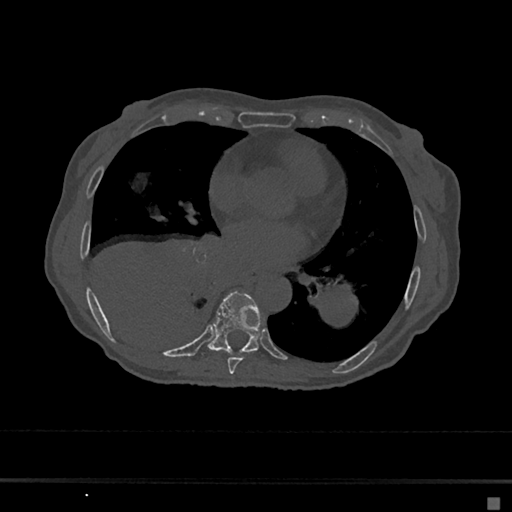
CT including the spine, one axial slice; position 344 of 797 along the scan axis; reconstruction kernel Br40s/3; 120 kVp; bone window (W 1800 / L 400 HU); 512 × 512 image matrix, field of view 360 × 360 mm. Female patient, age 68 years. Case-level facts recorded for this patient, not image findings: primary cancer: renal.
Annotated regions visible in this slice (semi-automatic segmentation, software-assisted and operator-edited):
- T7 vertebra: bounding box [x1, y1, x2, y2] px = [227, 357, 243, 374]
- T8 vertebra: [208, 291, 261, 355]